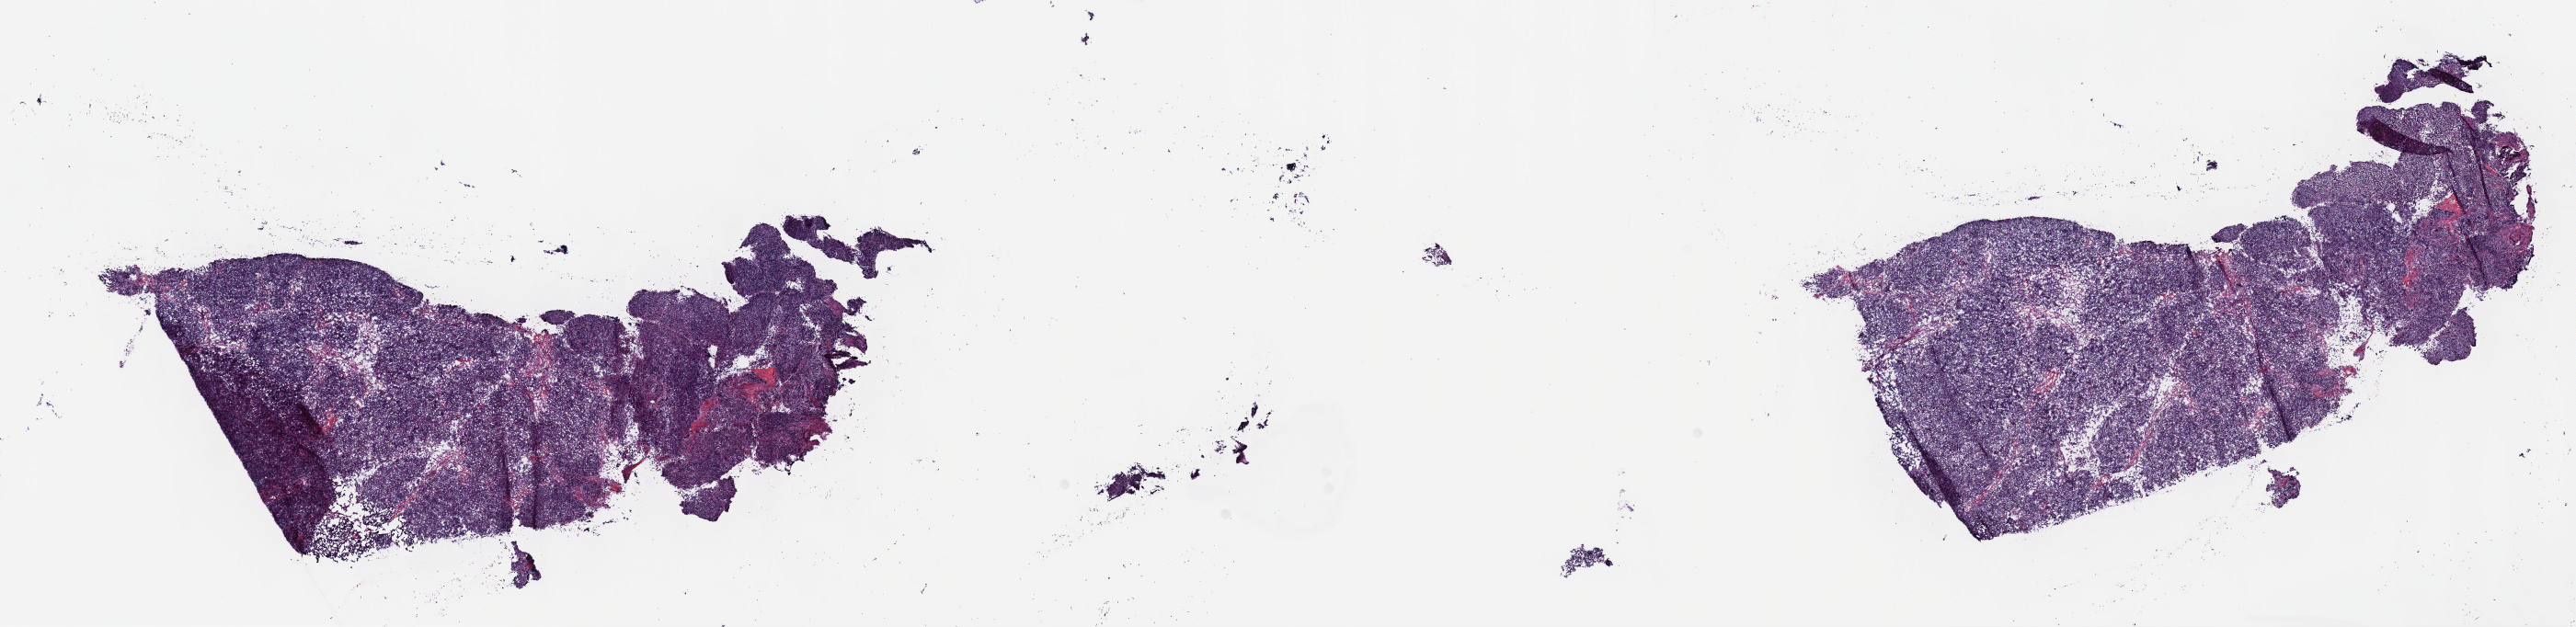
Whole-slide histology image, H&E-stained, shown as a low-resolution overview of the whole scanned area (about 22.7 x 5.5 mm). Frozen section from the top of the tissue portion. Sample: primary tumour, thymus. Female, age 76 years at initial diagnosis. Pathologist review of this section (percent, as recorded): tumour cells 100%, tumour nuclei 95%, normal cells 0%, stromal cells 0%, necrosis 0%. Inflammatory infiltration, as recorded: lymphocyte infiltration 0%, monocyte infiltration 0%, neutrophil infiltration 0%.
Pathologic diagnosis: Thymoma, type AB, malignant.